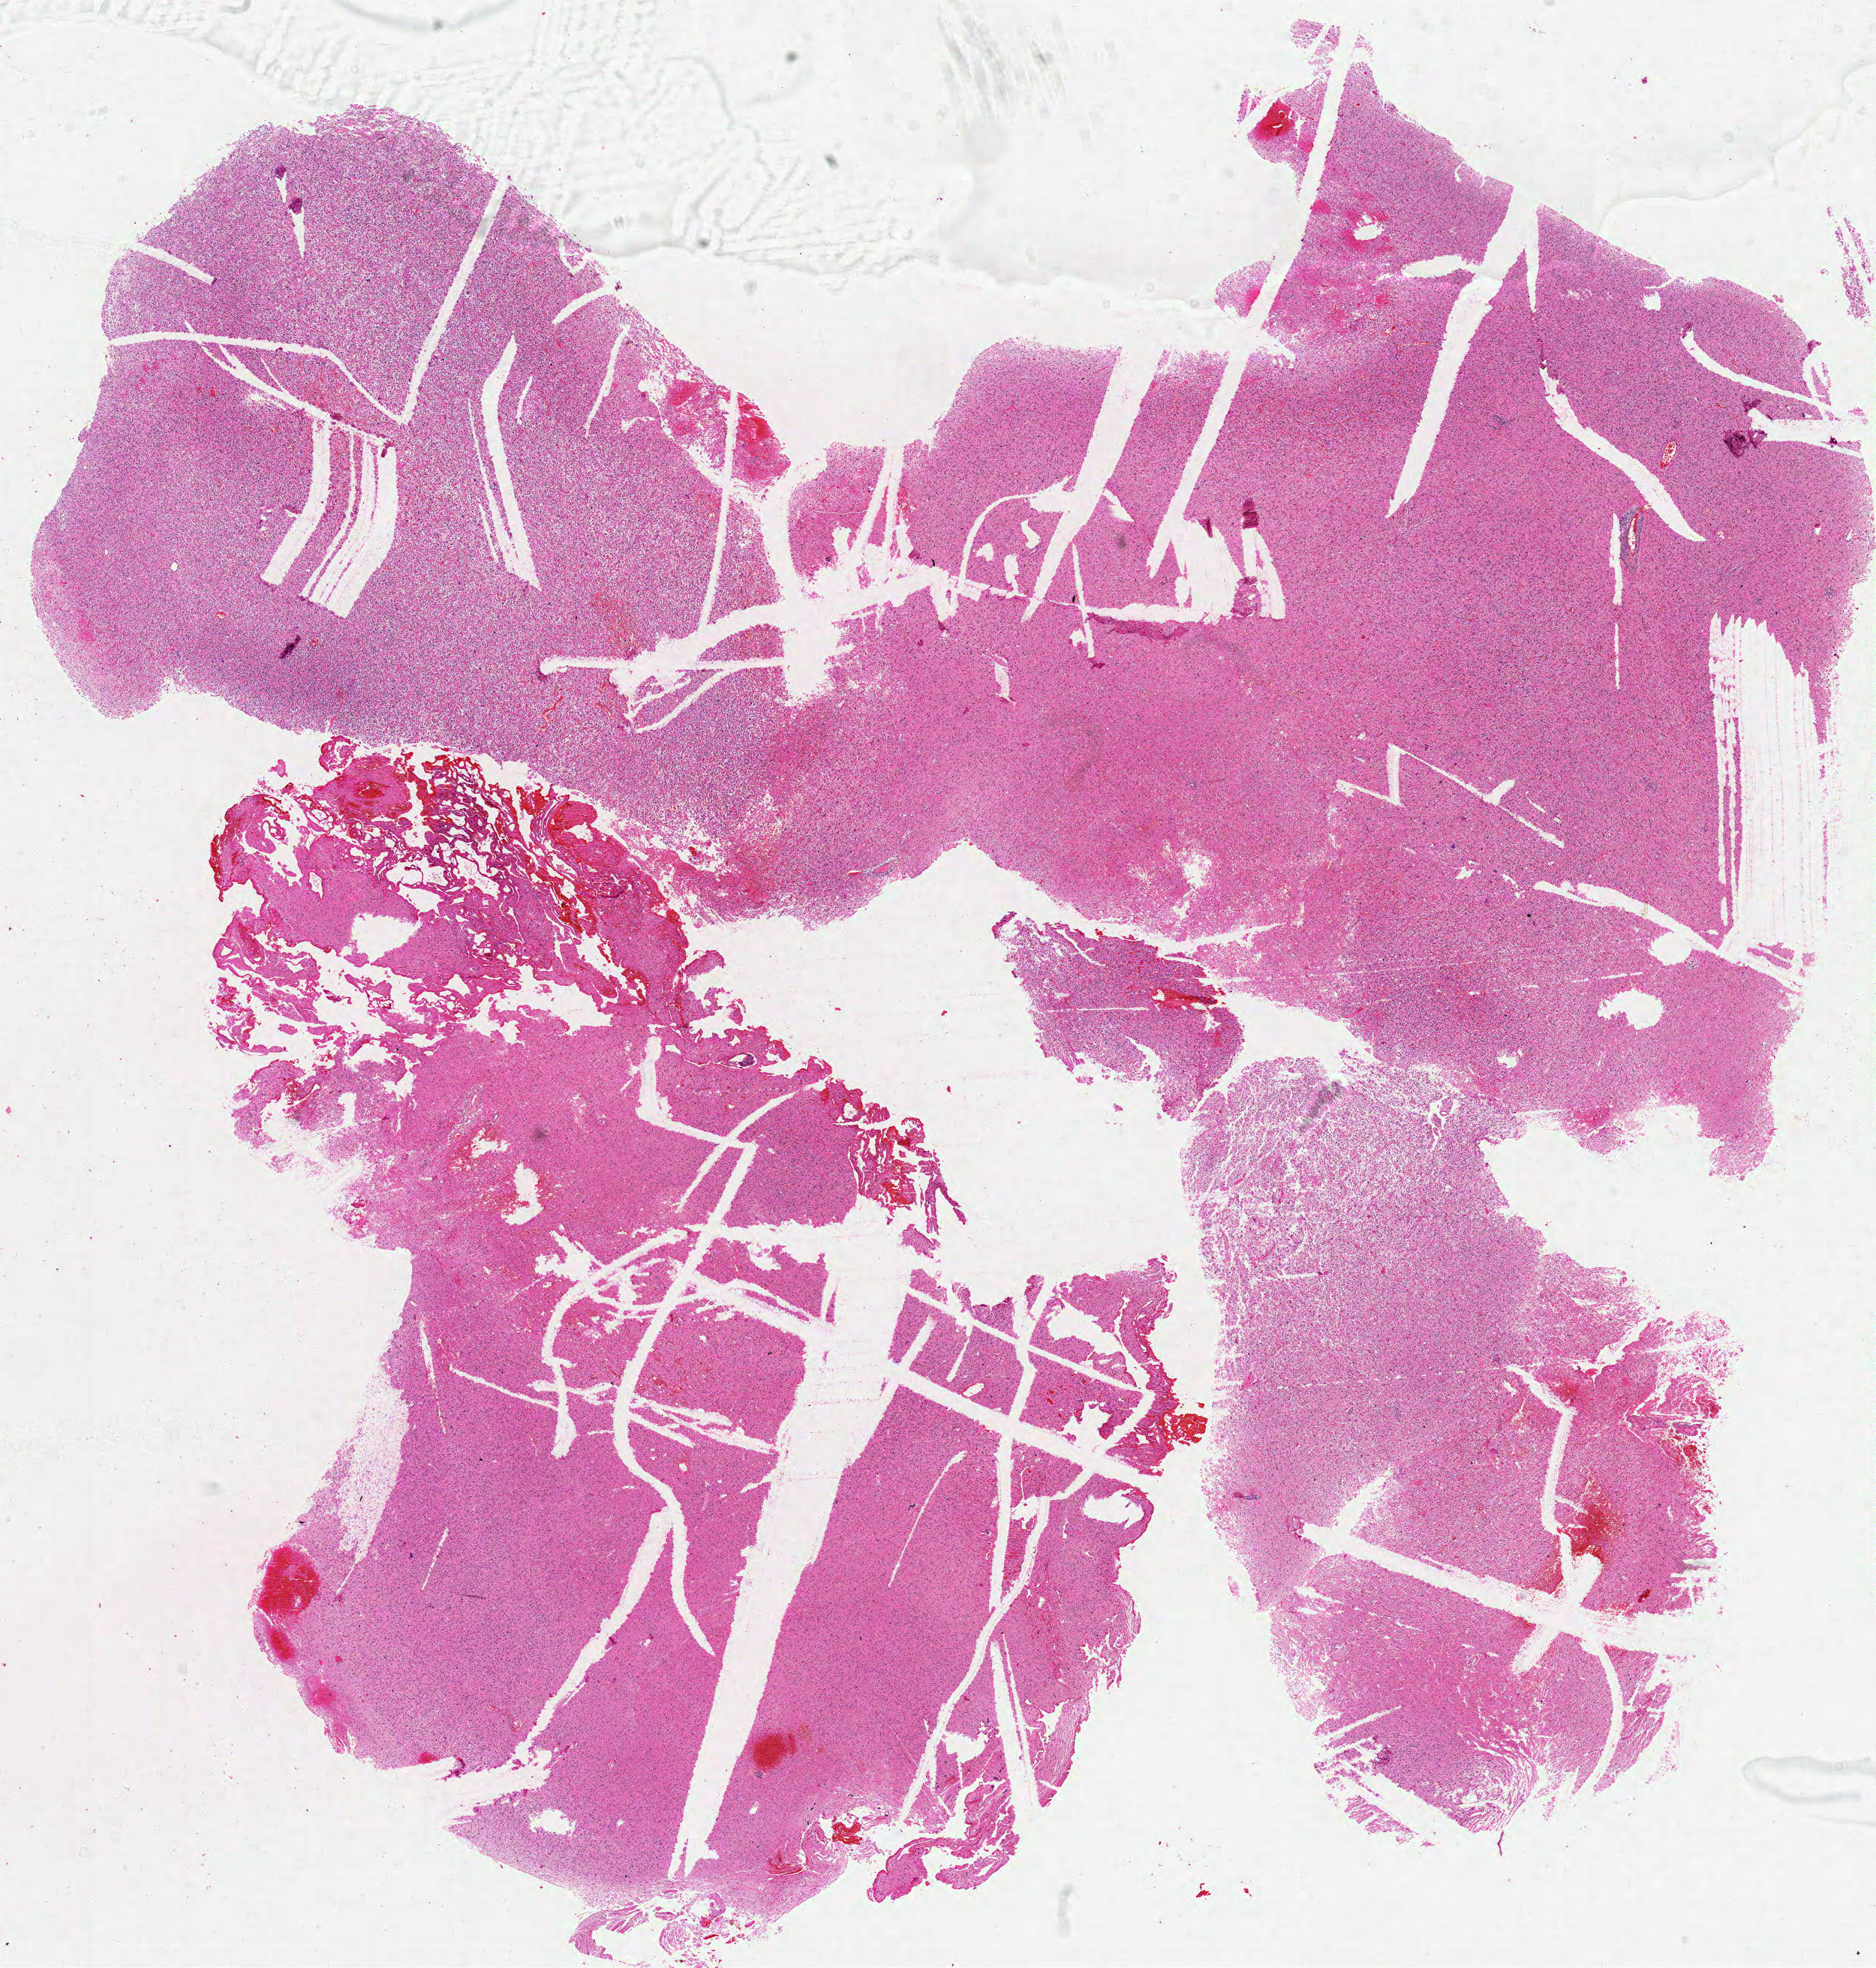
H&E-stained whole-slide image — shown as a low-resolution overview of the whole scanned area (about 20.0 x 21.0 mm, acquisition: 20x scan). Formalin-fixed paraffin-embedded (FFPE) diagnostic section. Primary tumour sample from the brain. Female, age 36 years at initial diagnosis.
Histologic diagnosis: Glioblastoma.